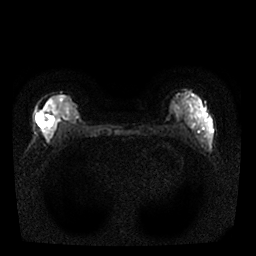
Breast MRI, one axial slice. Position 11 of 25 along the scan axis. Diffusion-weighted series; image 2 of 4 stored at this slice position (different b-values; order by instance number). 1.5 T. 4 mm slice thickness. 256 × 256 image matrix, field of view 310 × 310 mm. Female patient.
Outlined on this slice (expert manual segmentation):
- tumour on diffusion-weighted imaging: bounding box [x1, y1, x2, y2] px = [37, 112, 54, 134]